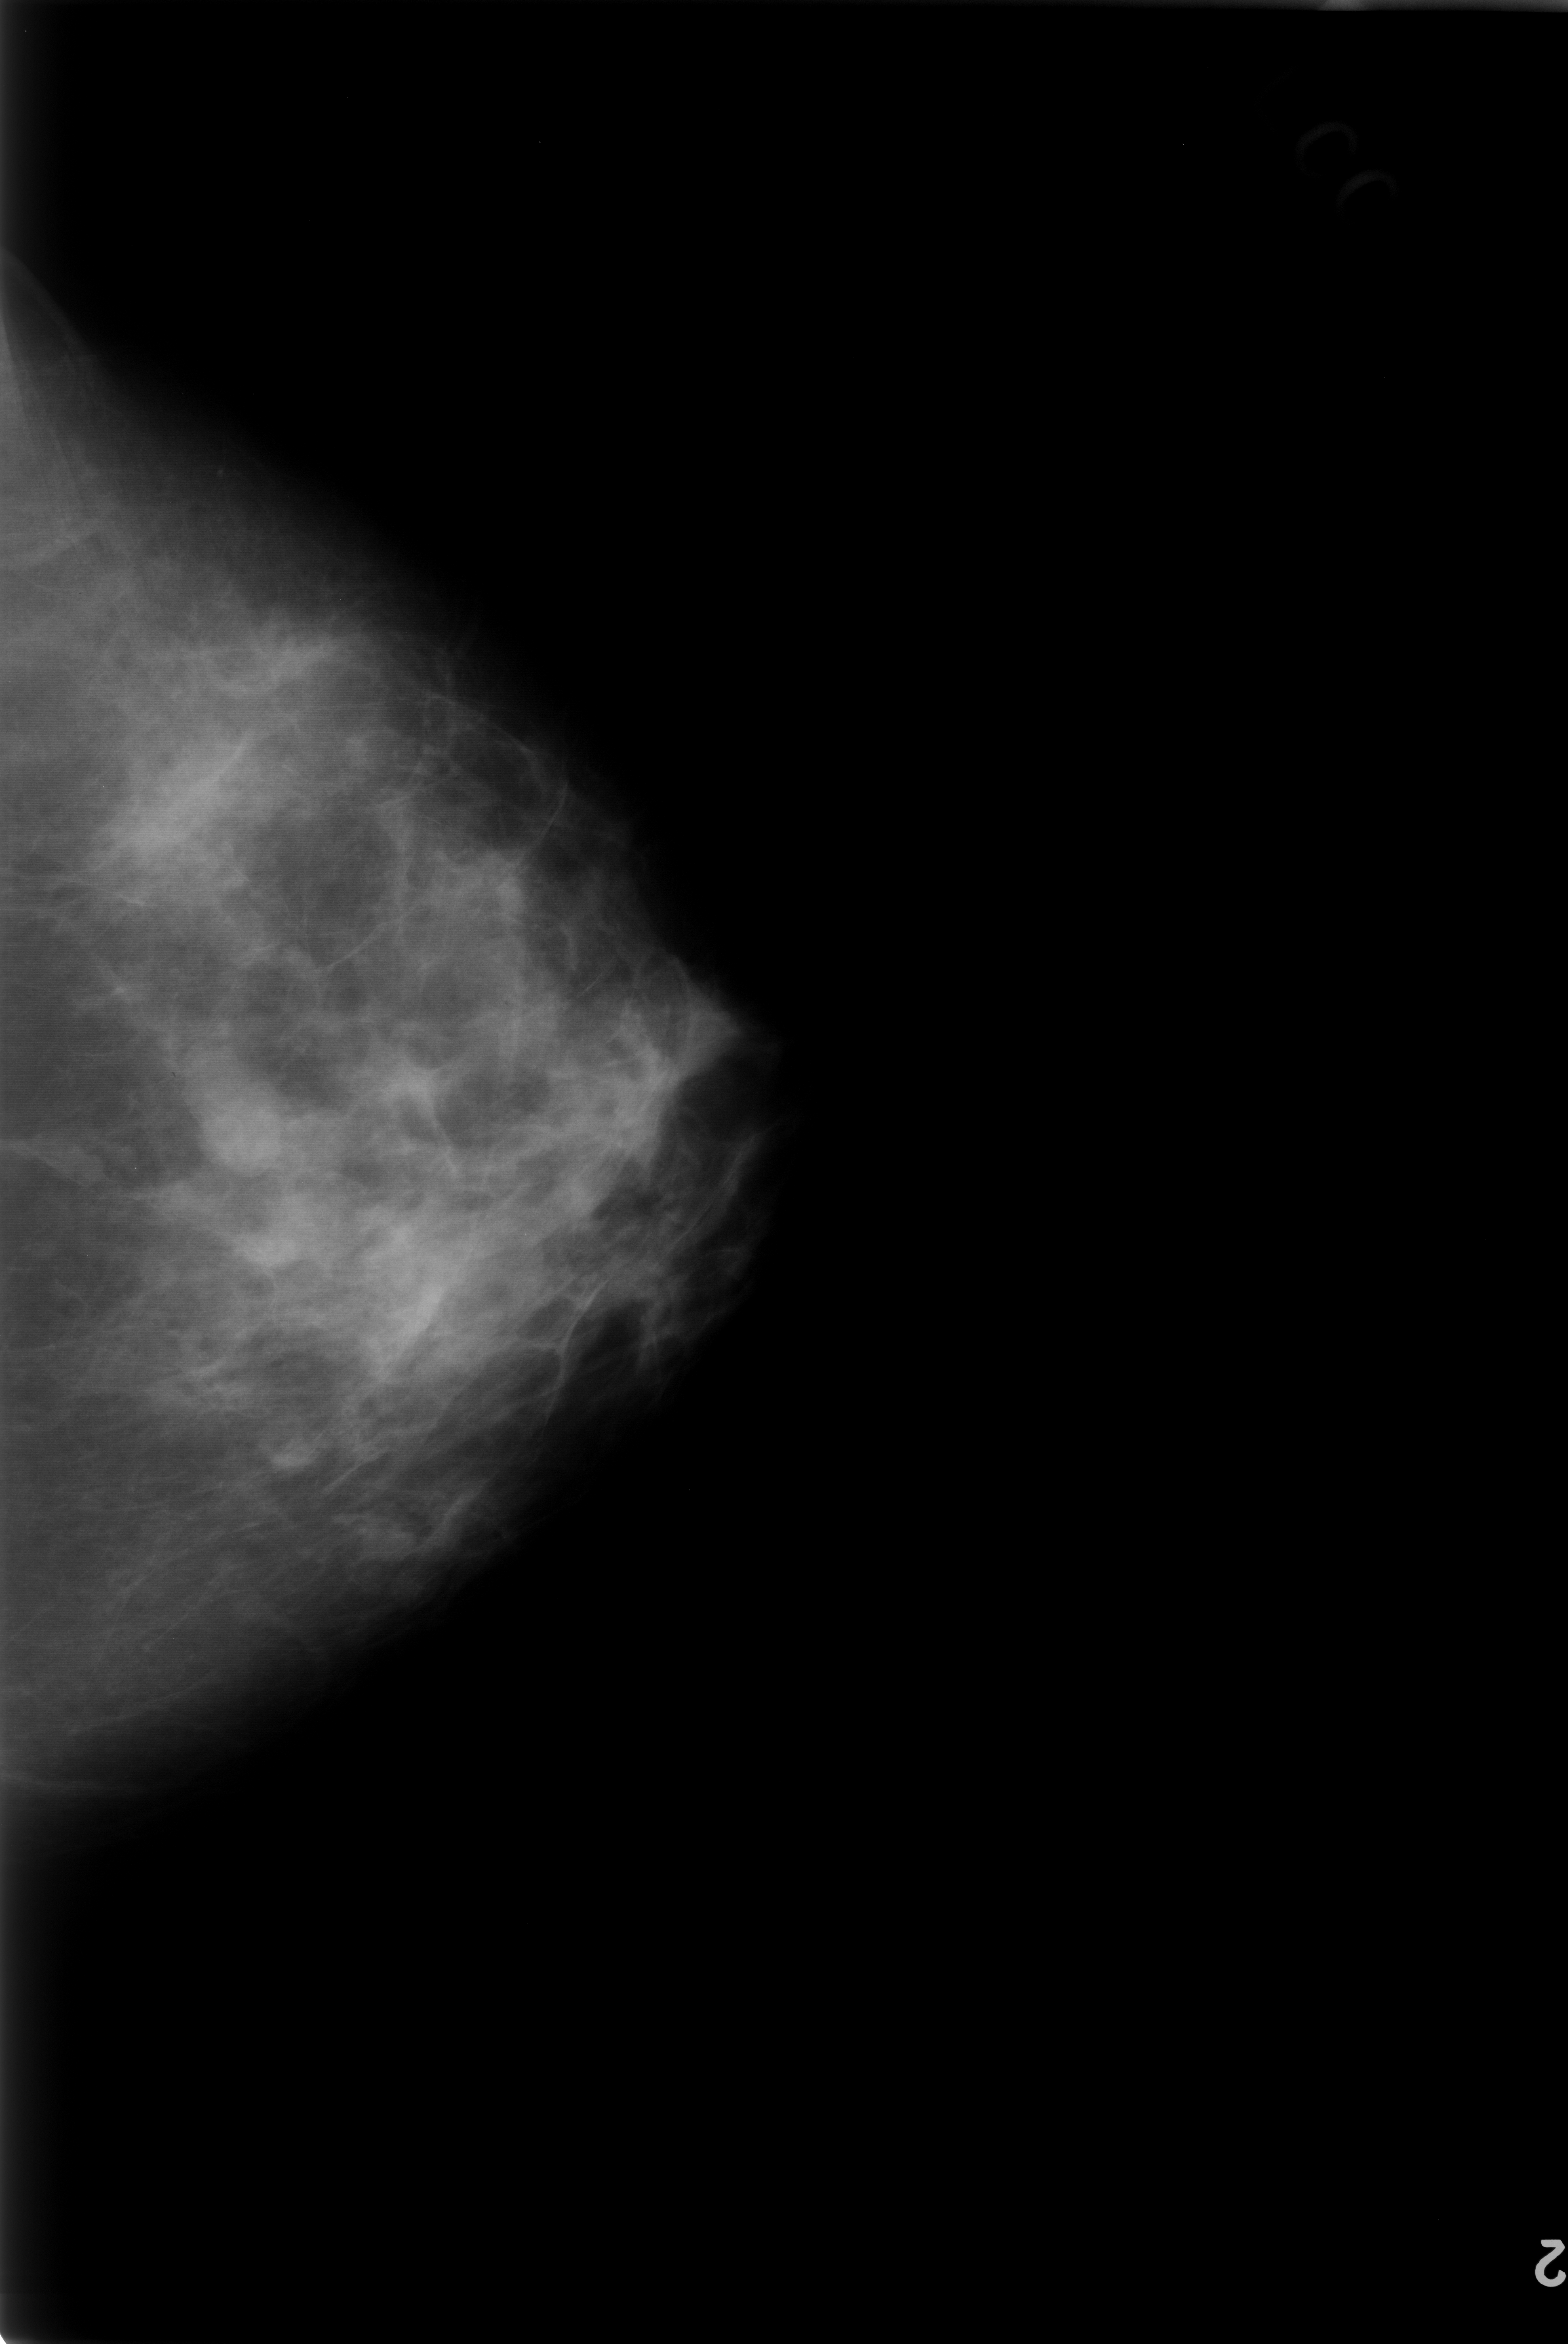
Scanned film-screen mammogram; left breast; craniocaudal (CC) view; breast composition: scattered fibroglandular densities (BI-RADS density category 2 of 4).
Finding: mass, shape lobulated, margins circumscribed; BI-RADS assessment category 3; pathology (as recorded): benign.